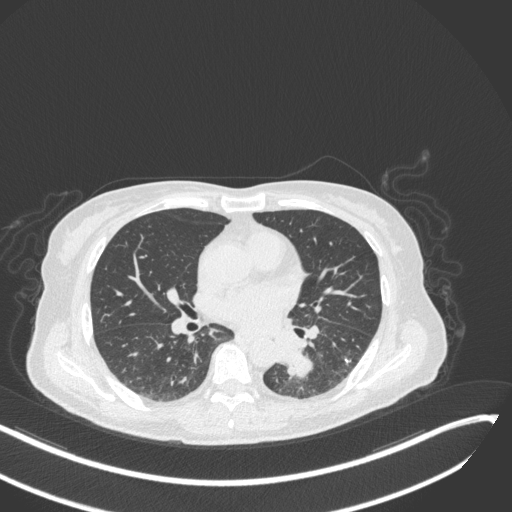
Chest CT, one axial slice. Position 133 of 342 along the scan axis. Lung window (W 1500 / L -600 HU). 1 mm slice thickness. 512 × 512 image matrix, field of view 400 × 400 mm. Patient: female, 64 years. Case-level facts recorded for this patient, not image findings: clinical TNM (as recorded): T3 N1 M1; histopathological grade: G3.
Annotated regions visible in this slice (rectangle marked by the reading radiologist):
- lung tumour (recorded histology: small cell carcinoma): bounding box (x1, y1, x2, y2) in pixels: (276, 347, 316, 388)